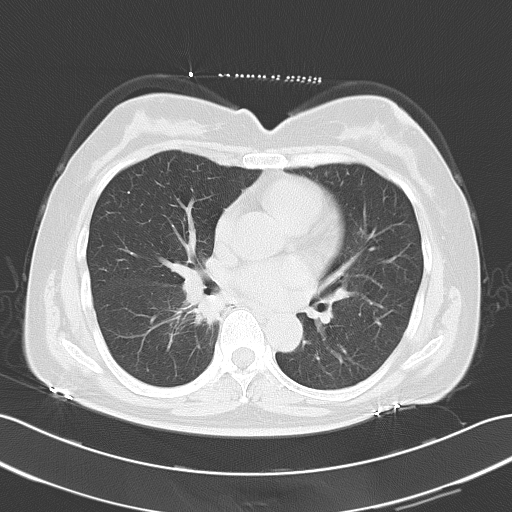
Chest CT, one axial slice; slice 29 of 55 in the series (ordered by position); reconstruction kernel B70f; lung window (W 1500 / L -600 HU); 5 mm slice thickness; 512 × 512 image matrix. Patient: female, 59 years. From the clinical record (not read from this slice): clinical TNM (as recorded): T1c N0 M1b.
Annotated regions visible in this slice (rectangle marked by the reading radiologist):
- lung tumour (recorded histology: adenocarcinoma): box from (x=187, y=291) to (x=227, y=332) px